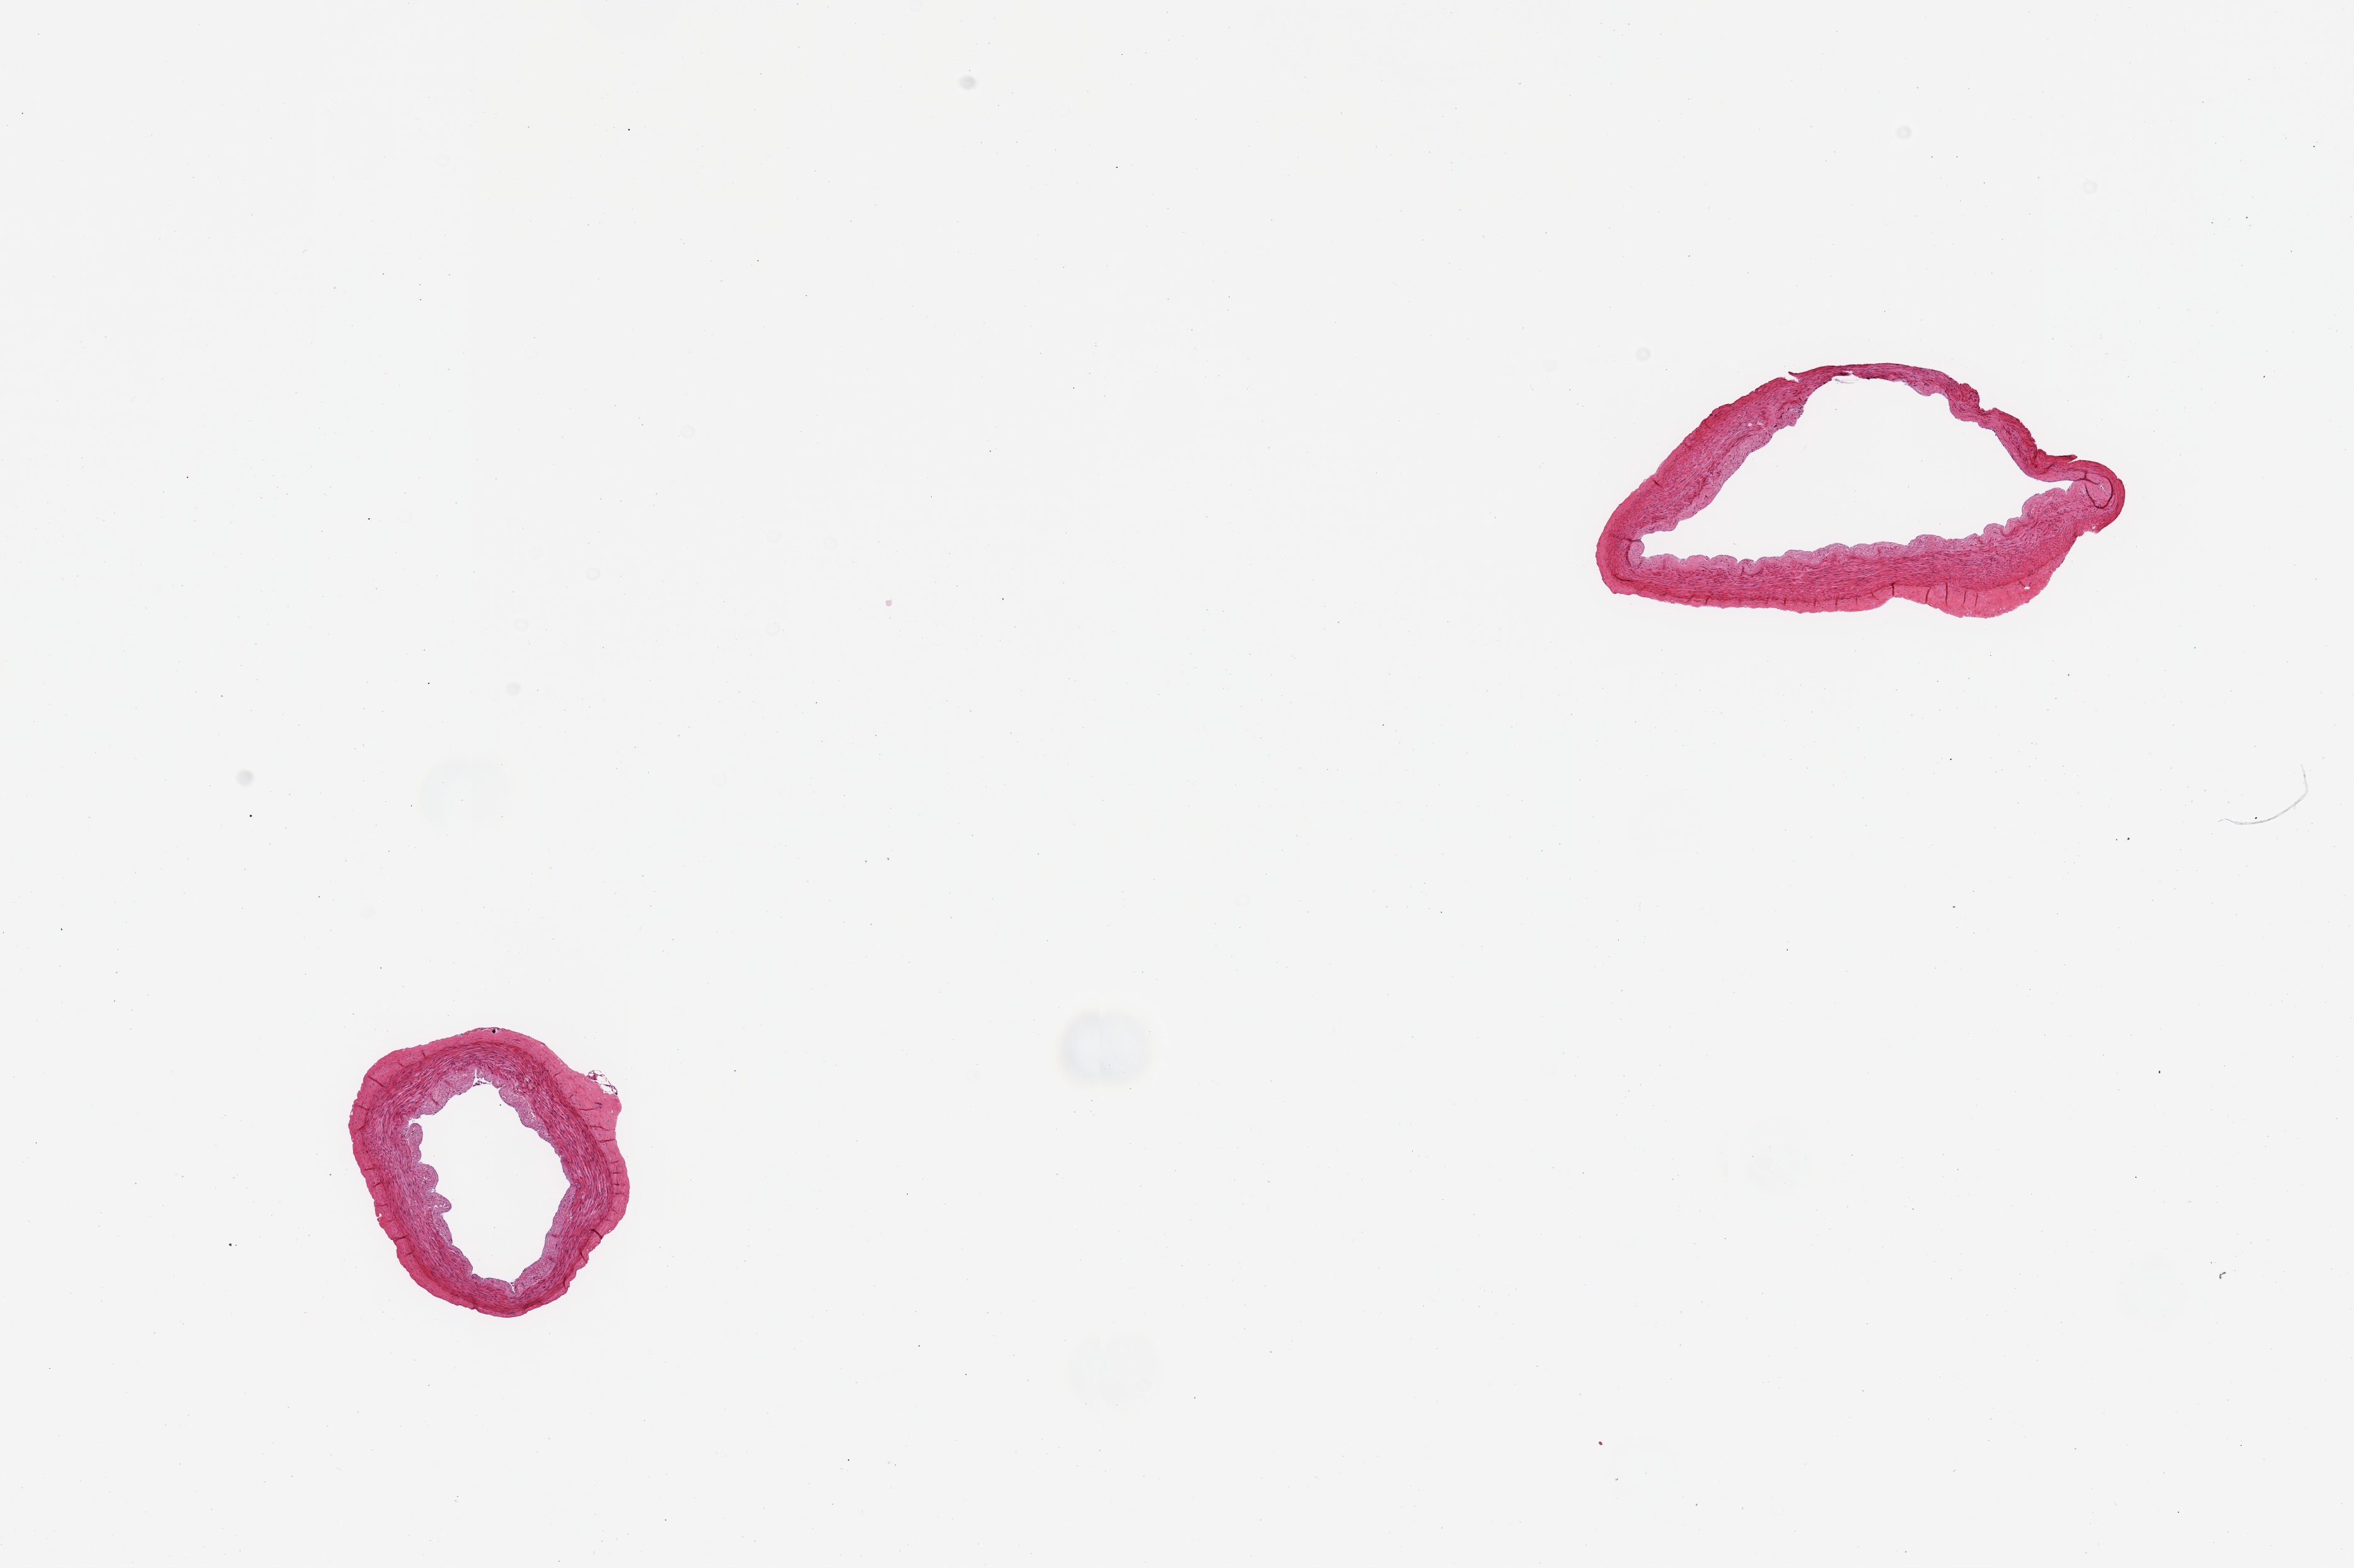
Whole-slide image, hematoxylin and eosin (H&E) stain, a low-resolution overview of the entire scanned area, about 14.8 x 9.8 mm; PAXgene-fixed paraffin-embedded (PFPE) section; target tissue: tibial artery; donor tissue sample. Donor: female.
• review note (as recorded): 2 pieces, no significant atherosis or adherent fat